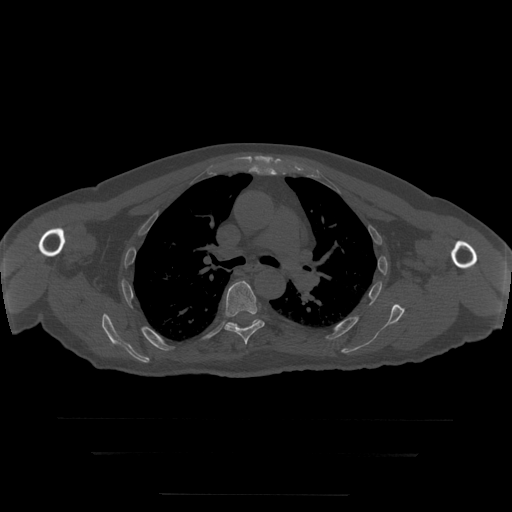
CT including the spine, one axial slice. Slice 205 of 397 in the series (ordered by position). 120 kVp. Bone window (W 1800 / L 400 HU). 1.25 mm slice thickness. 512 × 512 image matrix. Patient age 73 years. From the clinical record (not read from this slice): primary cancer: prostate.
Structures marked on this image (semi-automatic segmentation, software-assisted and operator-edited):
- T6 vertebra: box from (x=225, y=282) to (x=265, y=345) px
- T7 vertebra: (x=228, y=319)–(x=260, y=327)